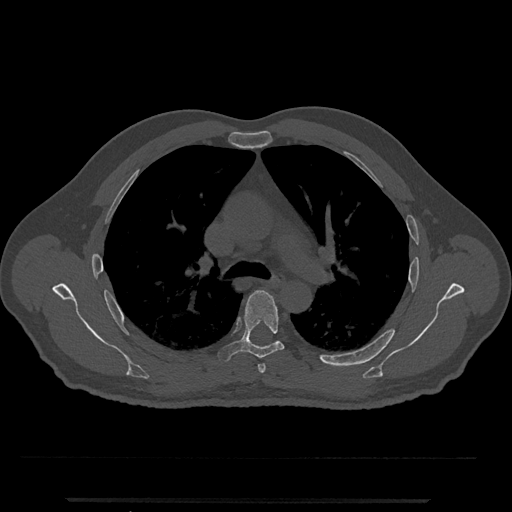
CT including the spine, one axial slice. Slice 795 of 797 in the series (ordered by position). Reconstruction kernel Br40s/3. Bone window (W 1800 / L 400 HU). 0.5 mm slice thickness. 512 × 512 image matrix. Male patient, age 63 years. Case-level facts recorded for this patient, not image findings: primary cancer: prostate.
Annotated regions visible in this slice (semi-automatically segmented with operator editing):
- T5 vertebra: bounding box [x1, y1, x2, y2] px = [217, 290, 285, 363]
- T6 vertebra: [271, 341, 278, 345]